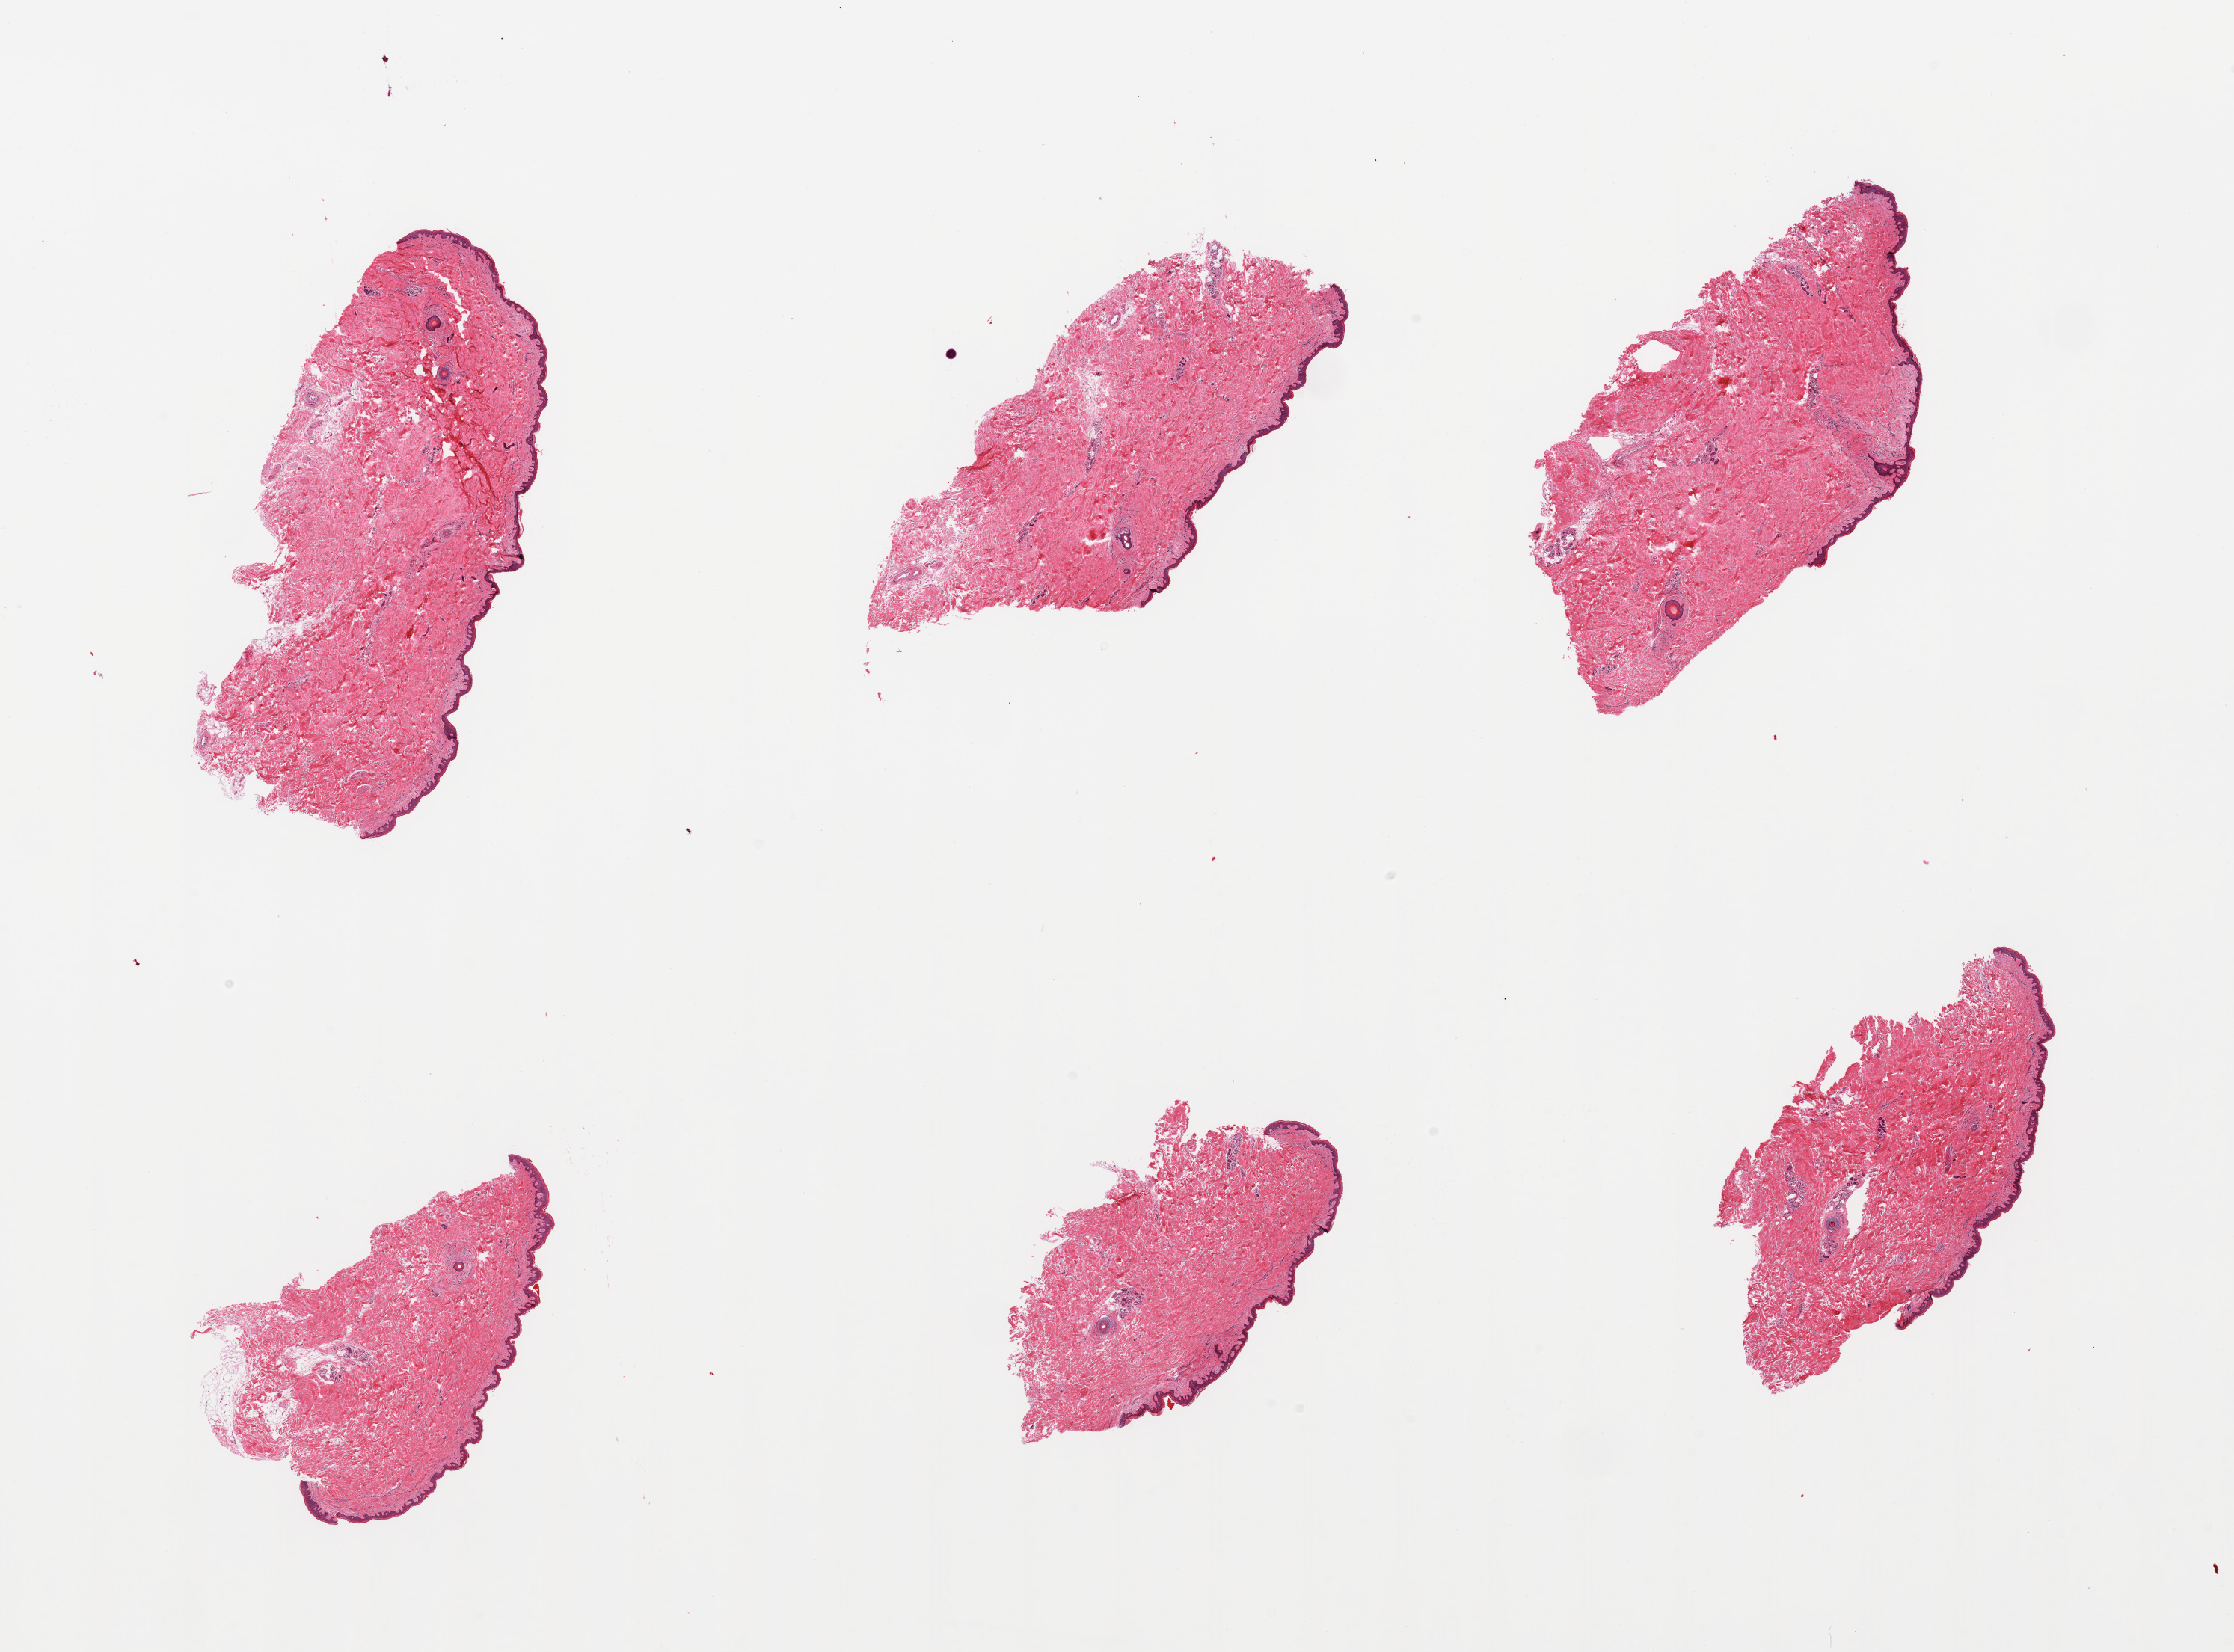
Haematoxylin and eosin whole-slide image, brightfield, a low-resolution overview of the entire scanned area, about 23.6 x 17.5 mm, PAXgene-fixed paraffin-embedded (PFPE) section, sampled site (target tissue): skin of suprapubic region, donor tissue sample. Male donor.
Reviewer comment on this tissue sample: 6 pieces; well trimmed;dermal fat <5%.